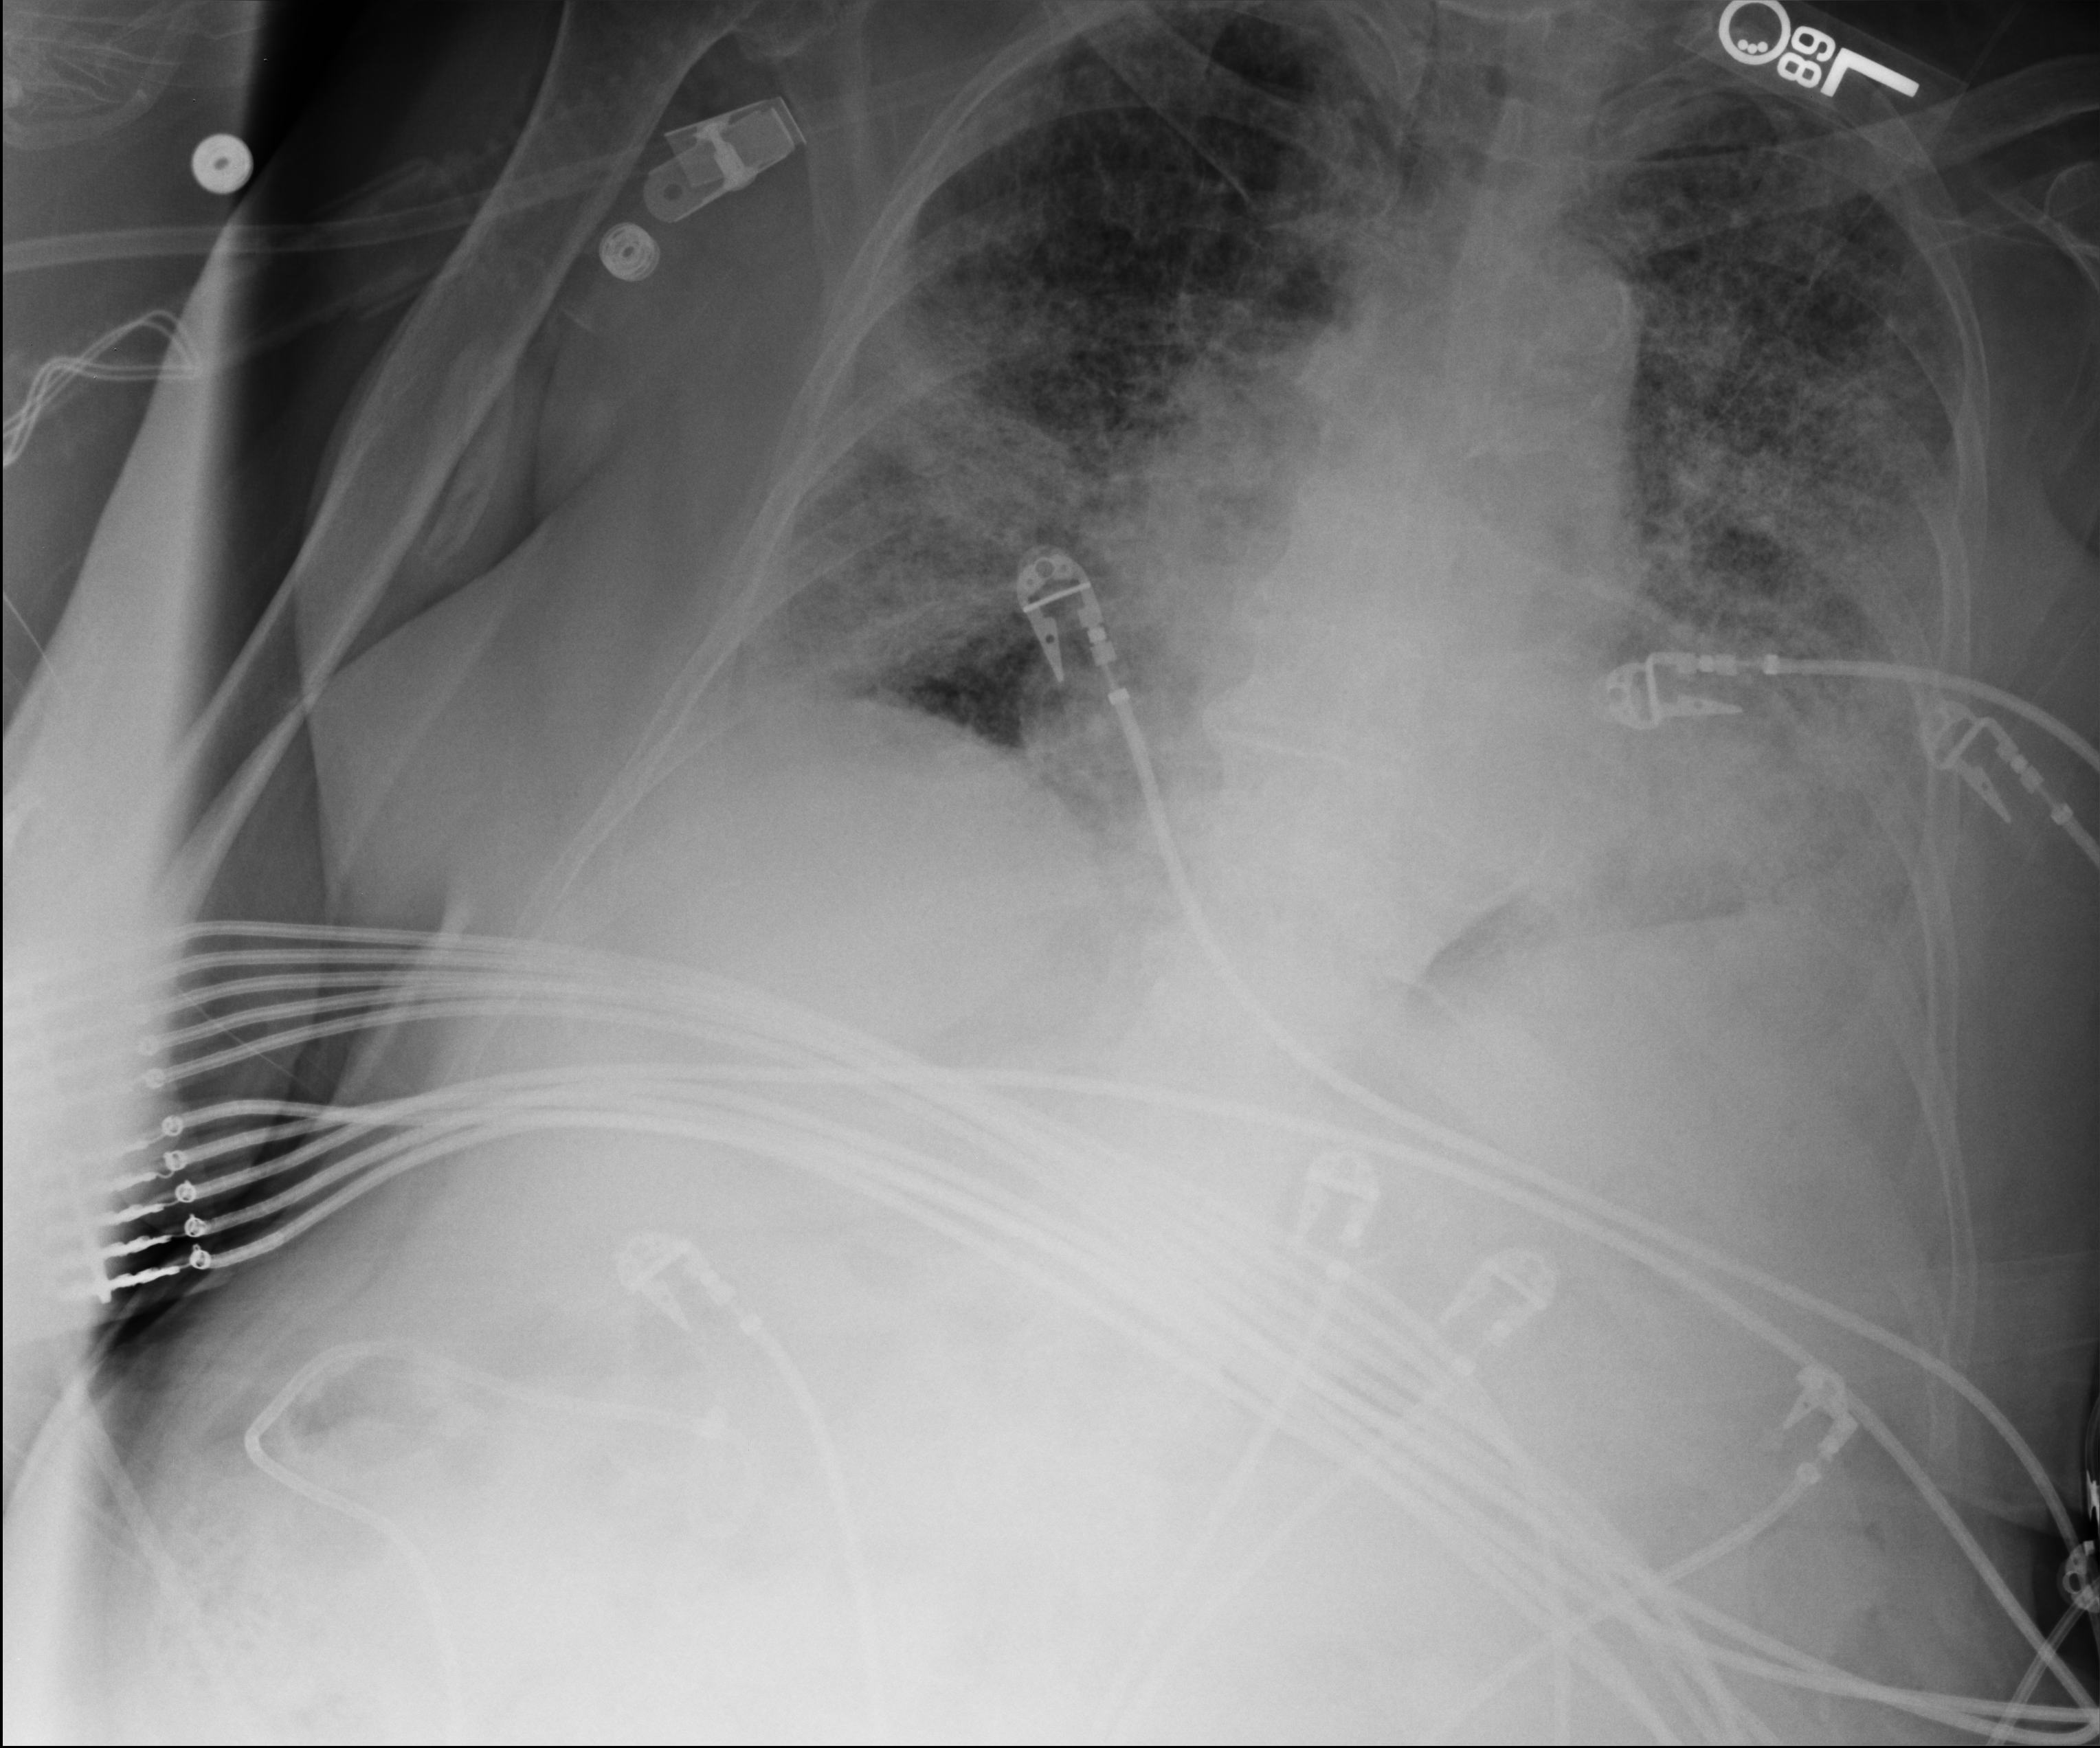
Bedside chest radiograph (computed radiography); anteroposterior (AP) projection. Female patient hospitalised with COVID-19, age 75–90 years.
Hospital-stay facts (about this admission, not read from this image; timing relative to this image not recorded):
- hypertension (admission record): yes
- chronic kidney disease (admission record): yes